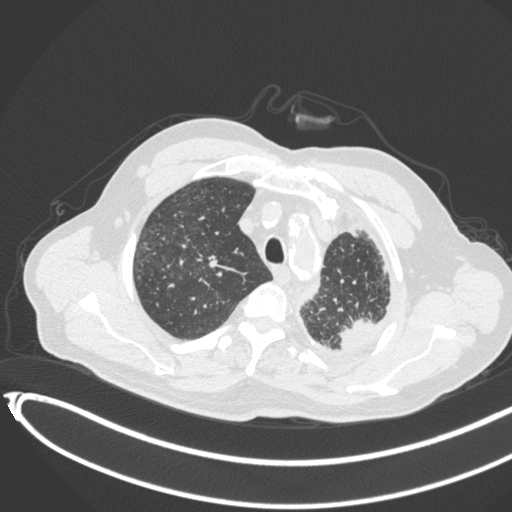
Chest CT, one axial slice. Position 354 of 451 along the scan axis. 120 kVp. Lung window (W 1500 / L -600 HU). 1 mm slice thickness. 512 × 512 image matrix, field of view 400 × 400 mm. Male patient, age 78 years. Case-level facts recorded for this patient, not image findings: clinical TNM (as recorded): T1c N0 M1.
Annotated regions visible in this slice (bounding box drawn by a radiologist):
- lung tumour (recorded histology: adenocarcinoma): bounding box (x1, y1, x2, y2) in pixels: (333, 315, 380, 356)